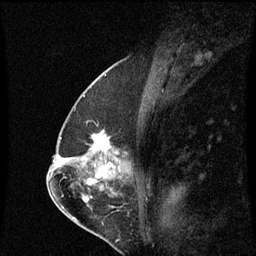
Breast MRI (dynamic contrast-enhanced), one sagittal slice. Slice 34 of 60 in the series (ordered by position). Dynamic contrast-enhanced series, image 2 of 3 at this slice position (ordered by acquisition). 1.5 T. TE 4.2 ms, TR 8.9 ms. 2 mm slice thickness. 256 × 256 image matrix, field of view 200 × 200 mm. Patient: female, 57 years. Case-level facts recorded for this patient, not image findings: setting: breast cancer imaged before/during neoadjuvant chemotherapy; receptor status: HR-positive, HER2-negative.
Annotated regions visible in this slice (semi-automatic segmentation, software-assisted and operator-edited):
- analysis volume of interest (the breast-tissue region the enhancement analysis was run in; not a lesion): bounding box <83,132,118,159> (left, top, right, bottom; pixels)
- tumour enhancement mask (voxels above the 70 % enhancement threshold inside the analysis volume of interest): <93,132,109,149>